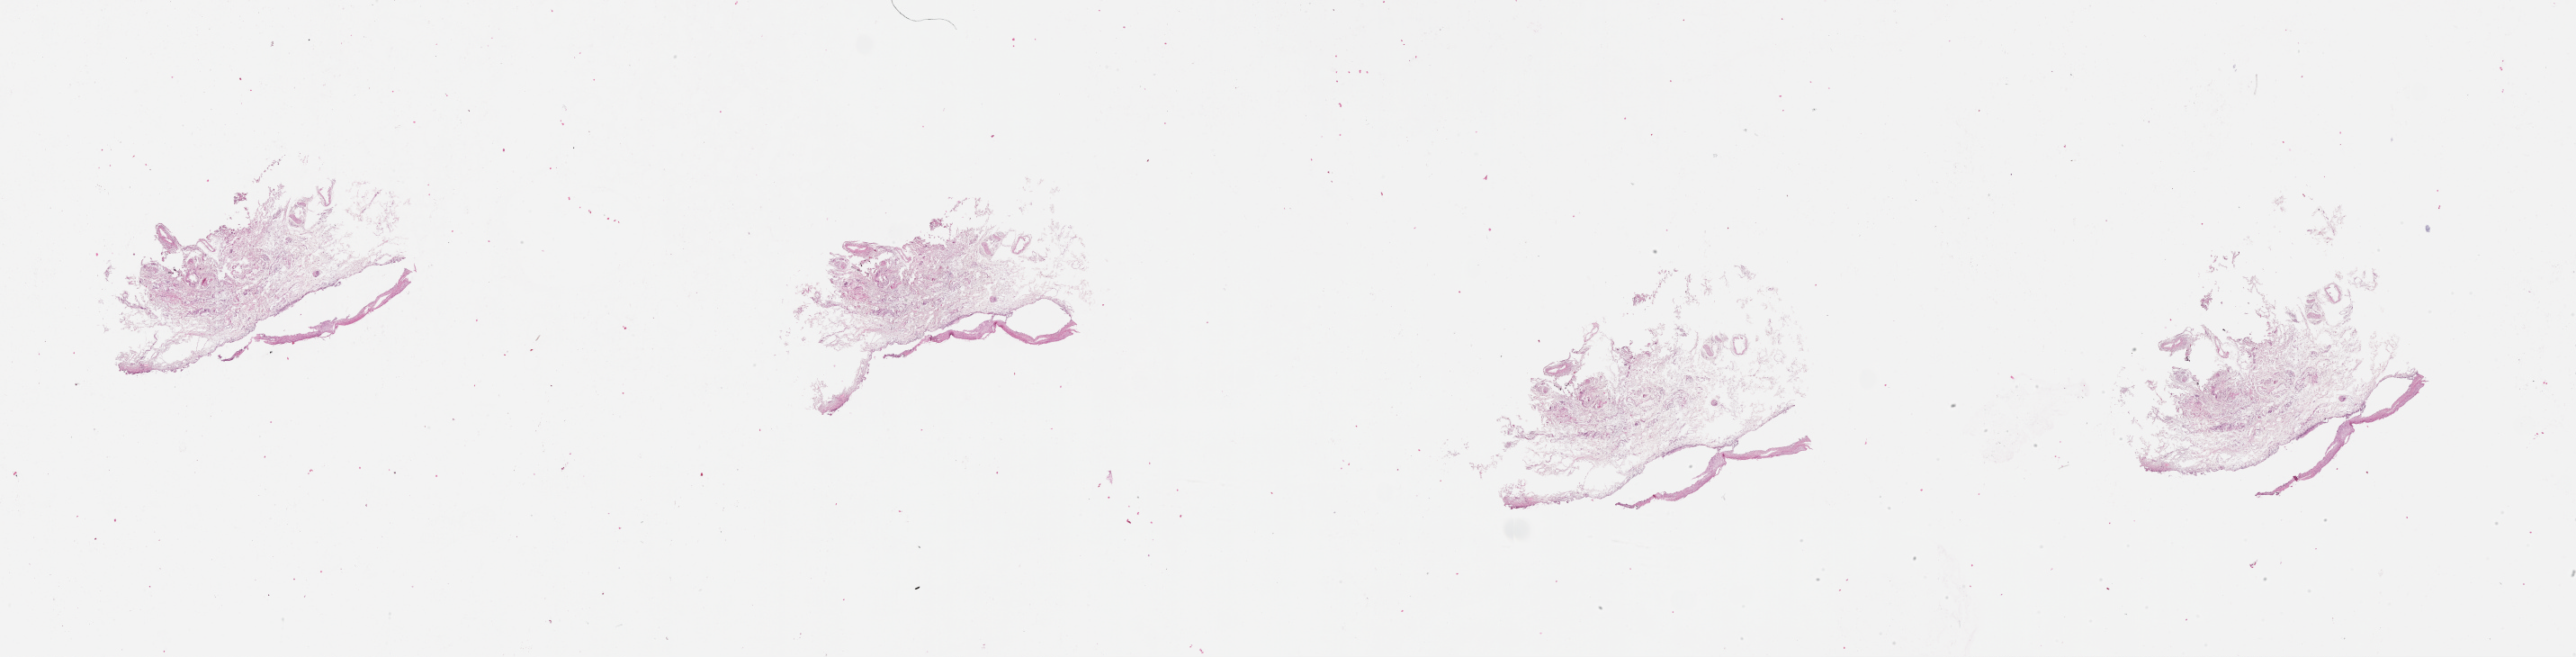
Whole-slide histology image, Hematoxylin and eosin (H&E) stained, whole scanned area (about 46.1 x 11.8 mm) shown as a low-resolution overview; head and neck, tissue type not recorded. Patient: male, age 70 years.
* patient diagnosis: Squamous cell carcinoma, NOS